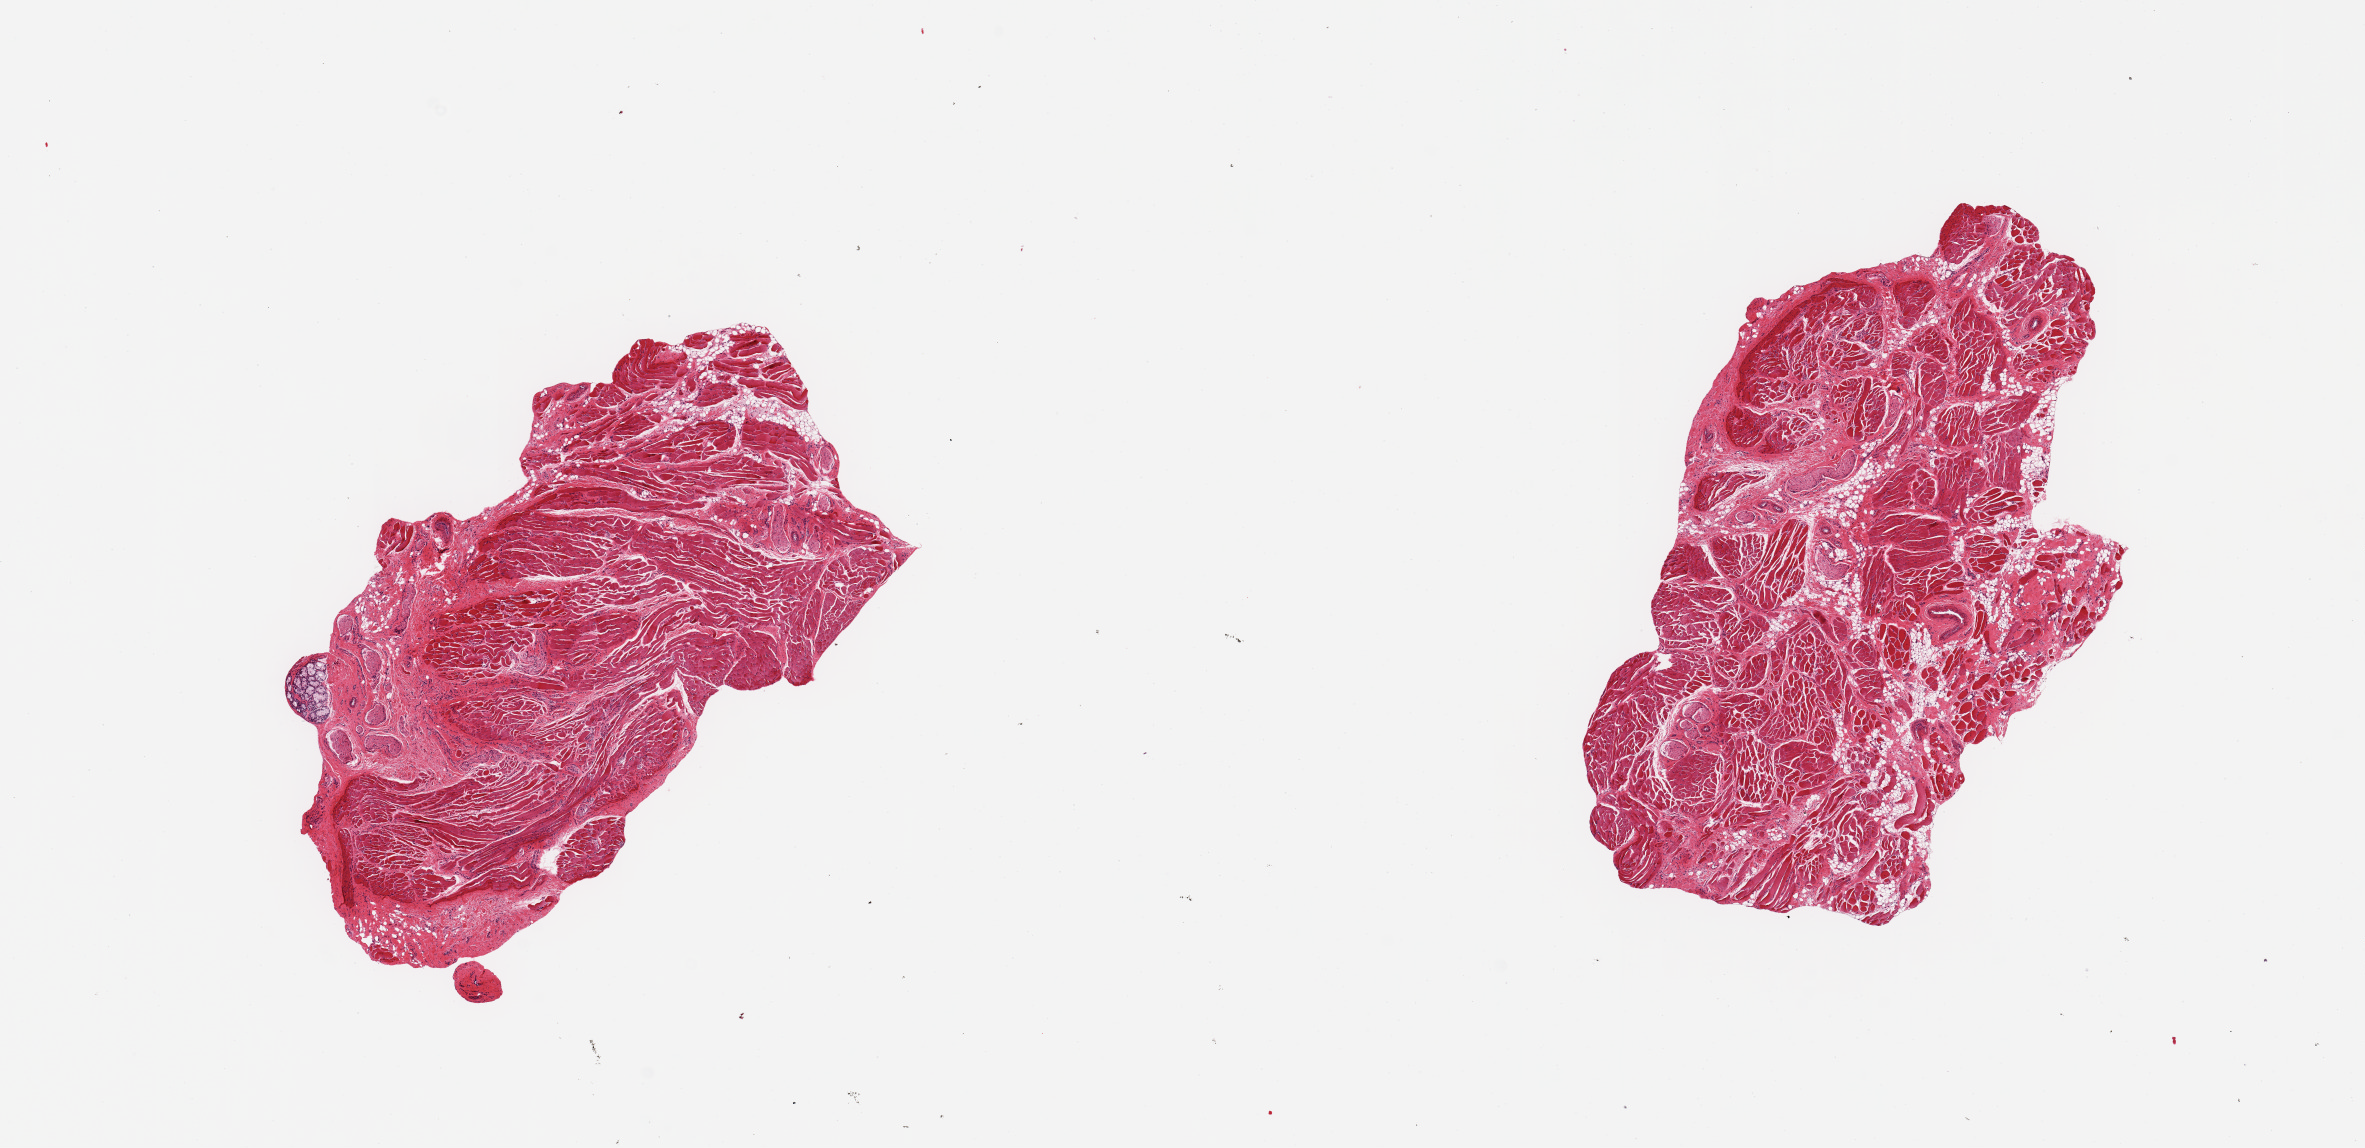
Whole-slide image, H&E stain — shown as a low-resolution overview of the whole scanned area (about 18.7 x 9.1 mm). PAXgene-fixed, paraffin-embedded tissue. Sampled site (target tissue): minor salivary gland. Tissue donor sample. Male donor.
* pathologist's review note for this sample: 2 pieces, skeletal muscle/stroma, only minute nubbin of glandular tissue (~0.5mm)